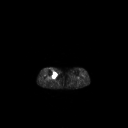
FDG PET of an extremity soft-tissue mass (from a PET/CT study), one axial slice. Slice 147 of 267 in the series (ordered by position). 128 × 128 image matrix. Female patient, age 65 years. Case-level facts recorded for this patient, not image findings: histological type: undifferentiated – high grade; grade: high; site of the primary tumour: right thigh.
Annotated regions visible in this slice (expert contour drawn on MRI and transferred to this co-registered scan by the dataset authors):
- gross tumour volume (mass): bounding box [x1, y1, x2, y2] px = [51, 70, 57, 78]